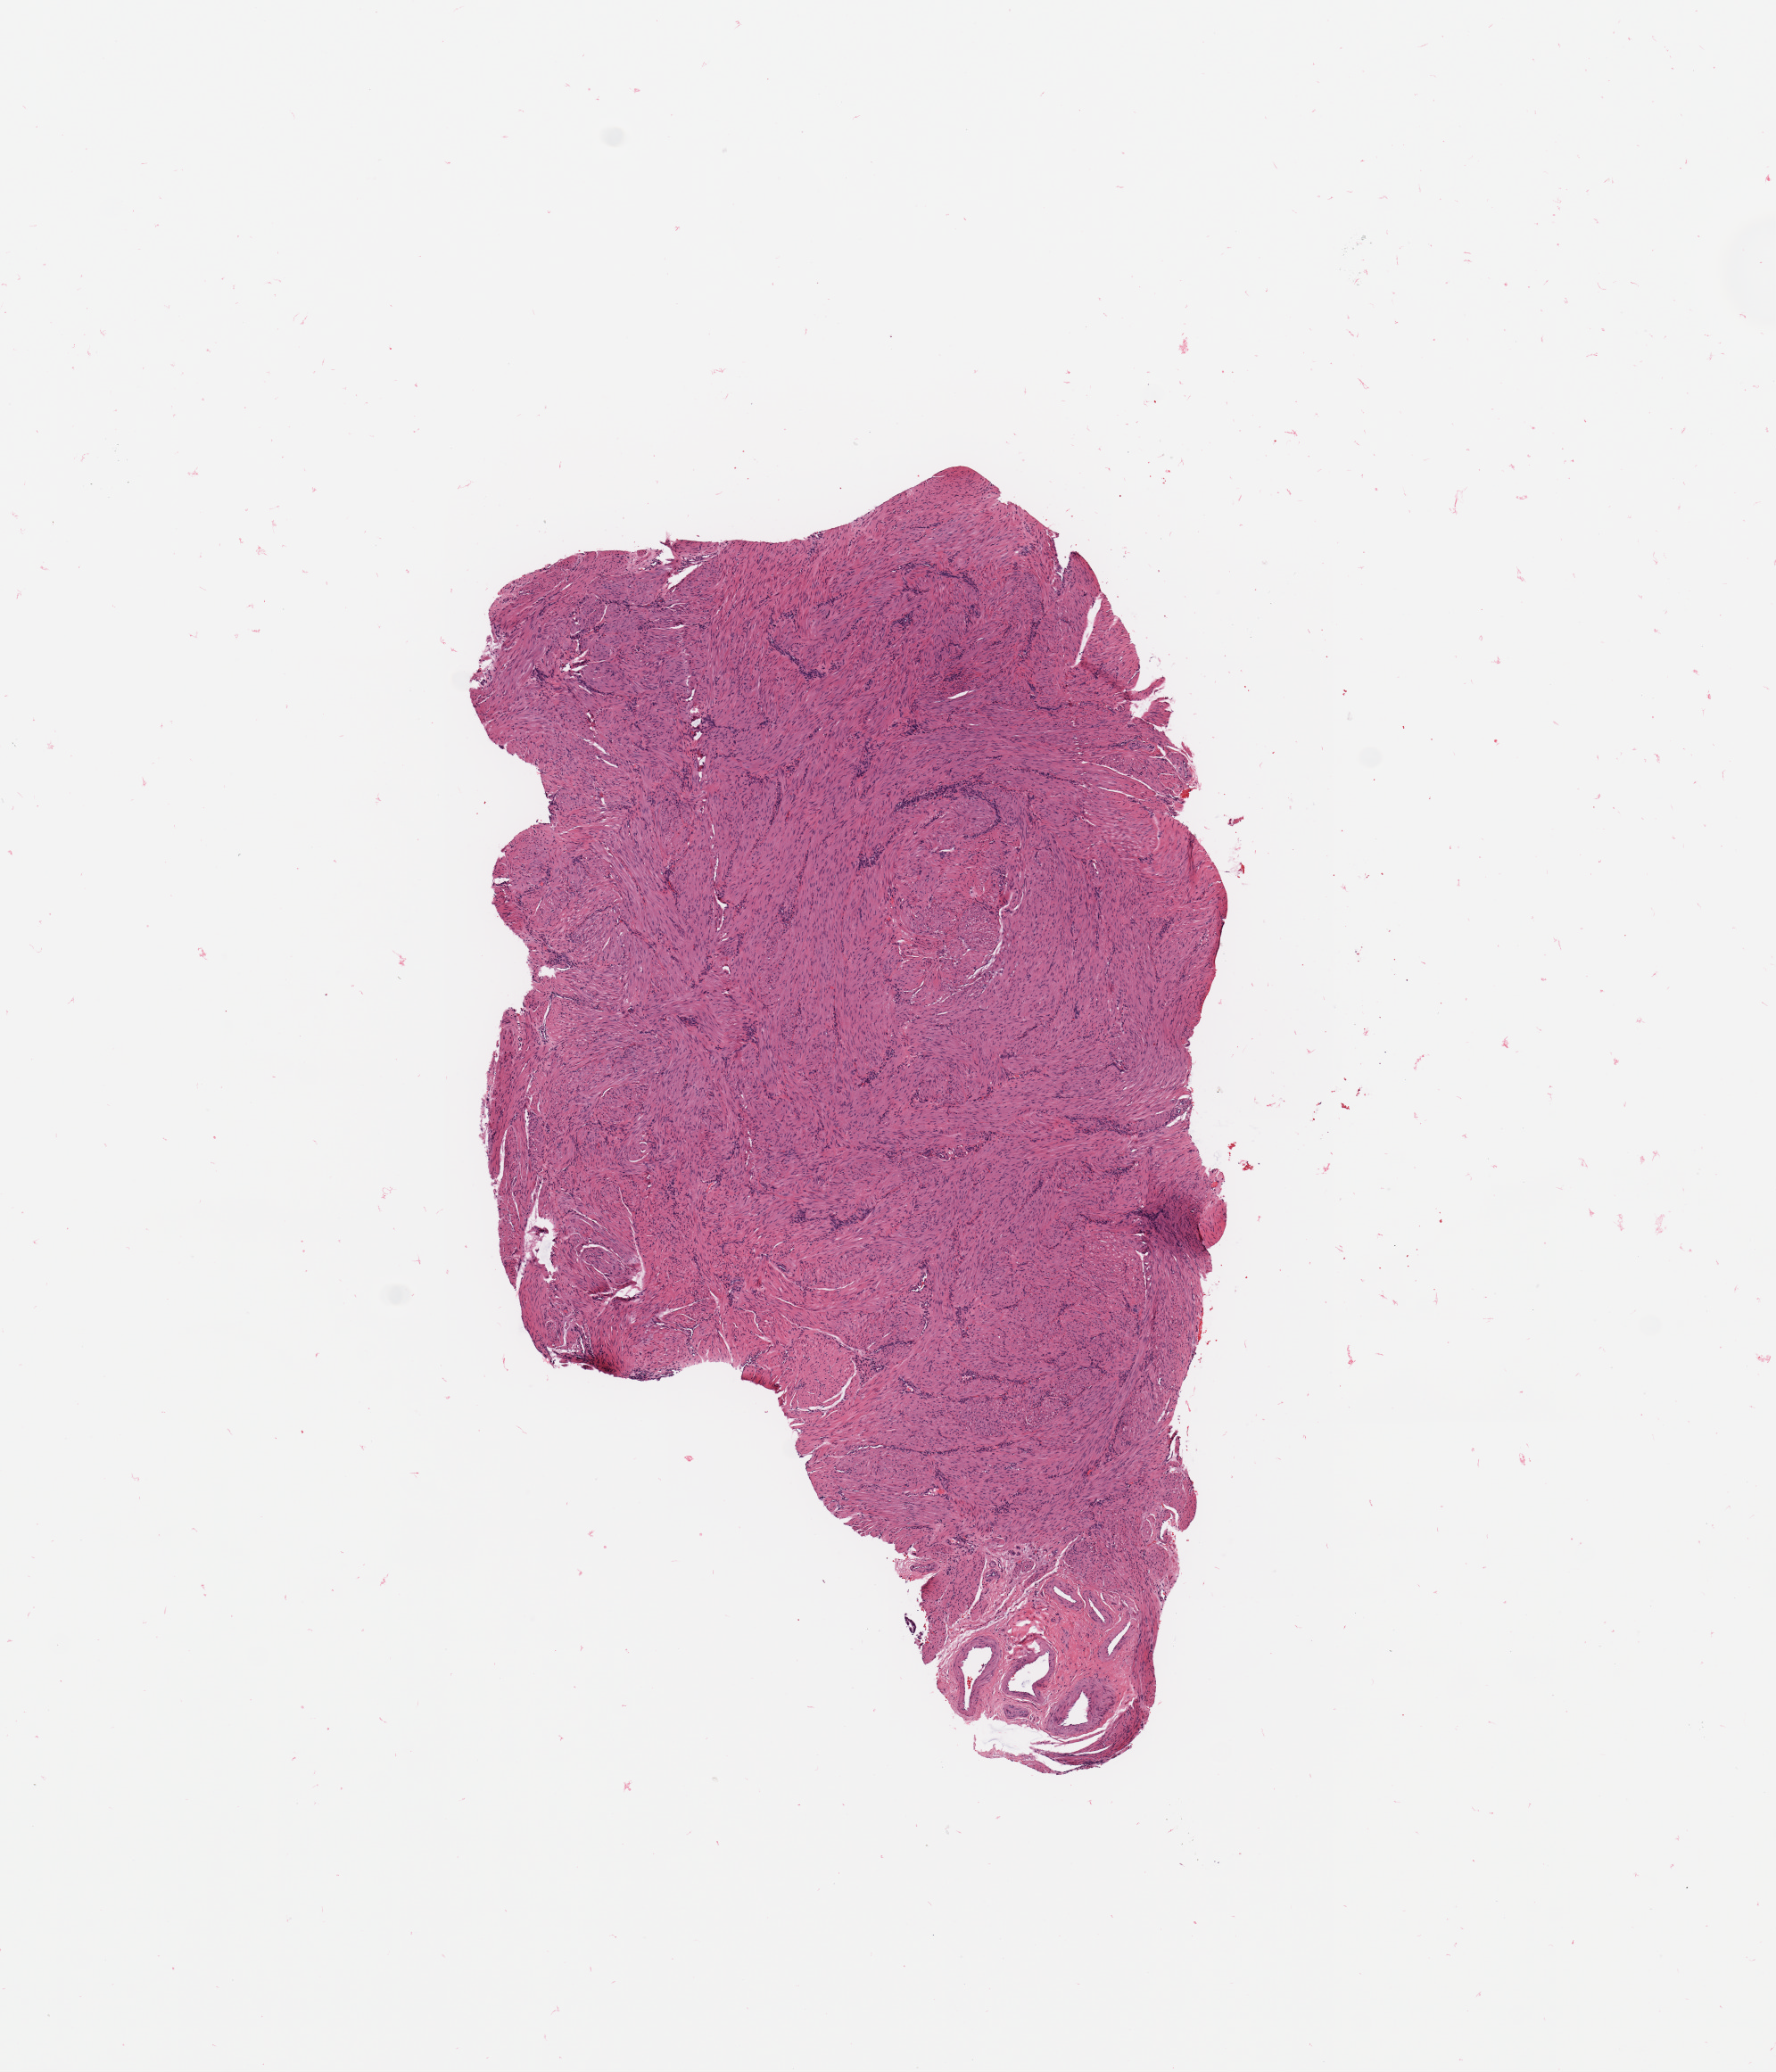
Whole-slide histology image, H&E-stained, shown as a low-resolution overview of the whole scanned area (about 7.9 x 9.2 mm, acquisition: 20x scan). Uterus, normal (non-tumour) tissue. 56-year-old female patient.
* this section: normal (non-tumour) tissue from the same patient
* patient diagnosis: Endometrioid adenocarcinoma, NOS